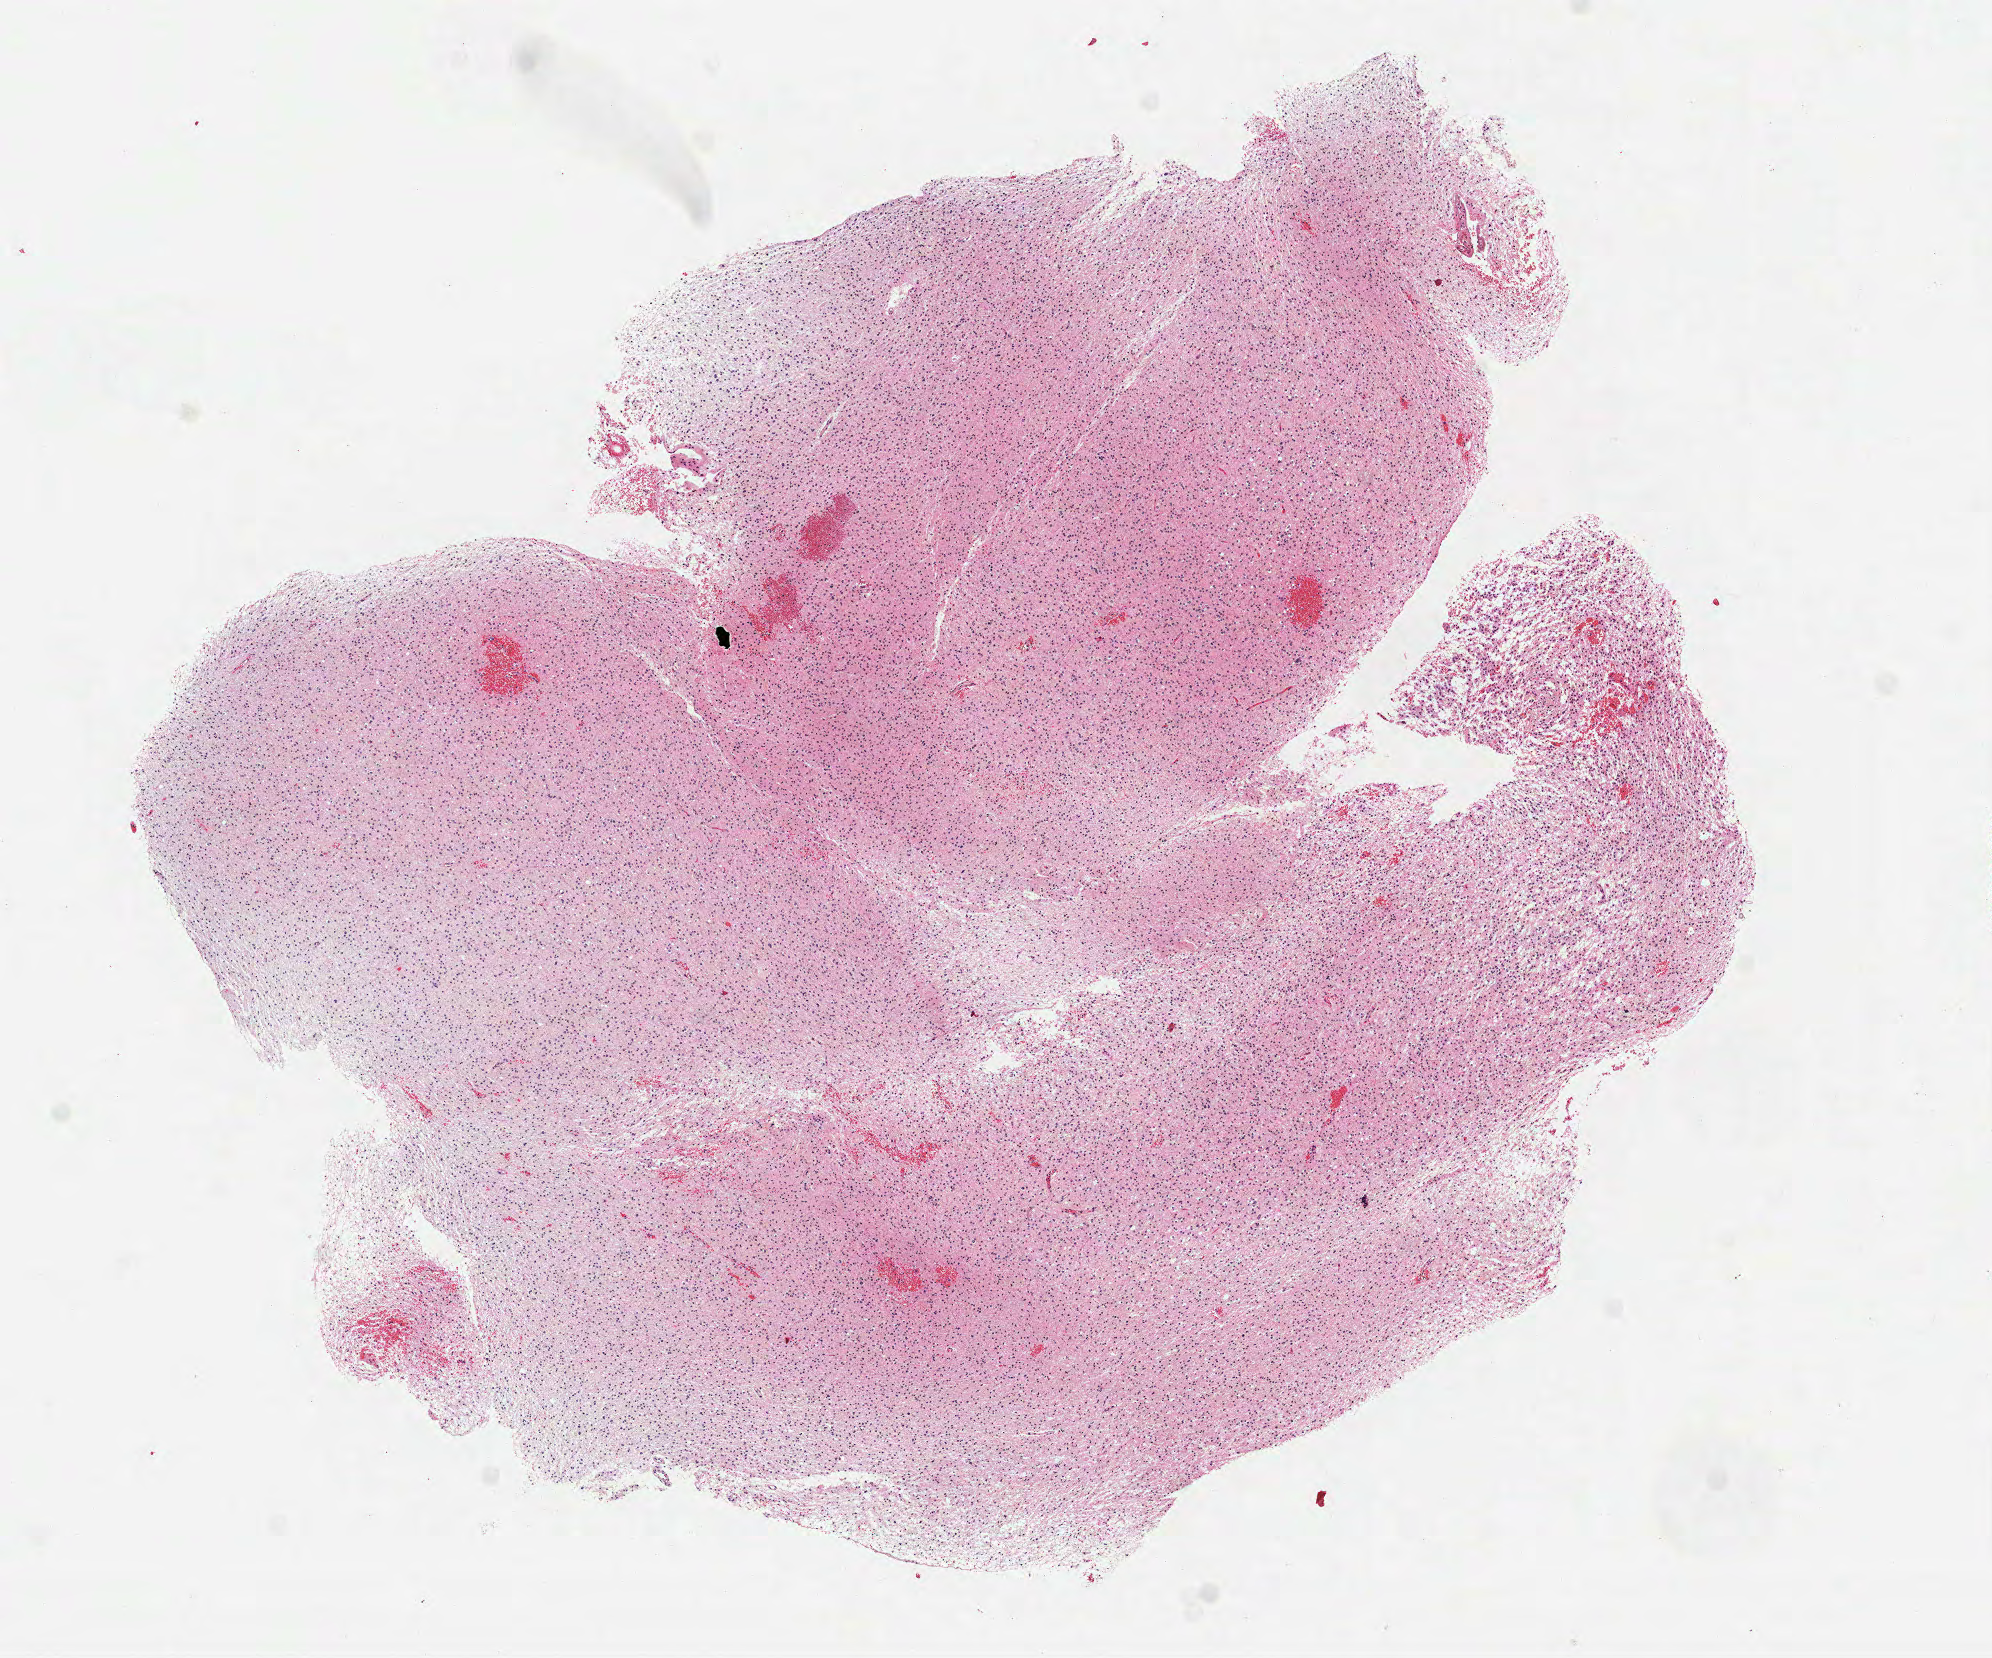
Digitized H&E-stained tissue section (whole slide) — a low-resolution overview of the entire scanned area, about 8.0 x 6.7 mm; frozen section from the top of the tissue portion; primary tumour sample from the brain. Male patient; age at initial diagnosis 35 years. Histologic grade: G2 (moderately differentiated). Composition of this section per pathologist review: tumour cells 100%, tumour nuclei 80%, normal cells 0%, stromal cells 0%, necrosis 0%.
• diagnosis: Oligodendroglioma, NOS